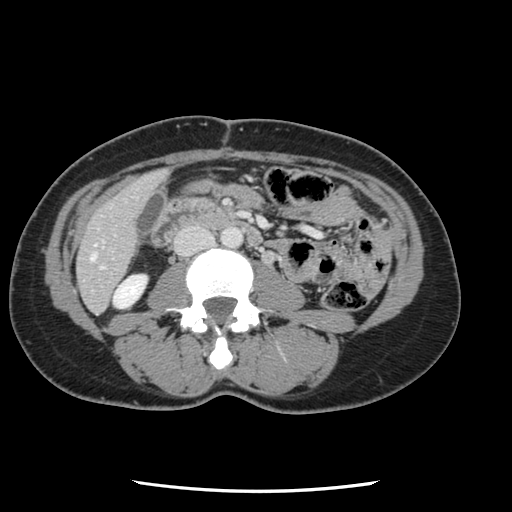
Contrast-enhanced abdominal CT, one axial slice. Position 20 of 134 along the scan axis. 120 kVp. Intravenous contrast given. Soft-tissue window (W 400 / L 40 HU). 2.5 mm slice thickness. 512 × 512 image matrix, field of view 330 × 330 mm. Female patient, age 43 years. From the clinical record (not read from this slice): diagnosis: colorectal cancer liver metastases, imaged before liver resection; multiple liver metastases: yes; largest metastasis: 3.4 cm.
Outlined on this slice (manually delineated by an expert):
- hepatic veins: bounding box <91,253,96,260> (left, top, right, bottom; pixels)
- liver: <79,172,165,312>
- planned liver remnant (the part of the liver to remain after resection): <78,172,165,312>